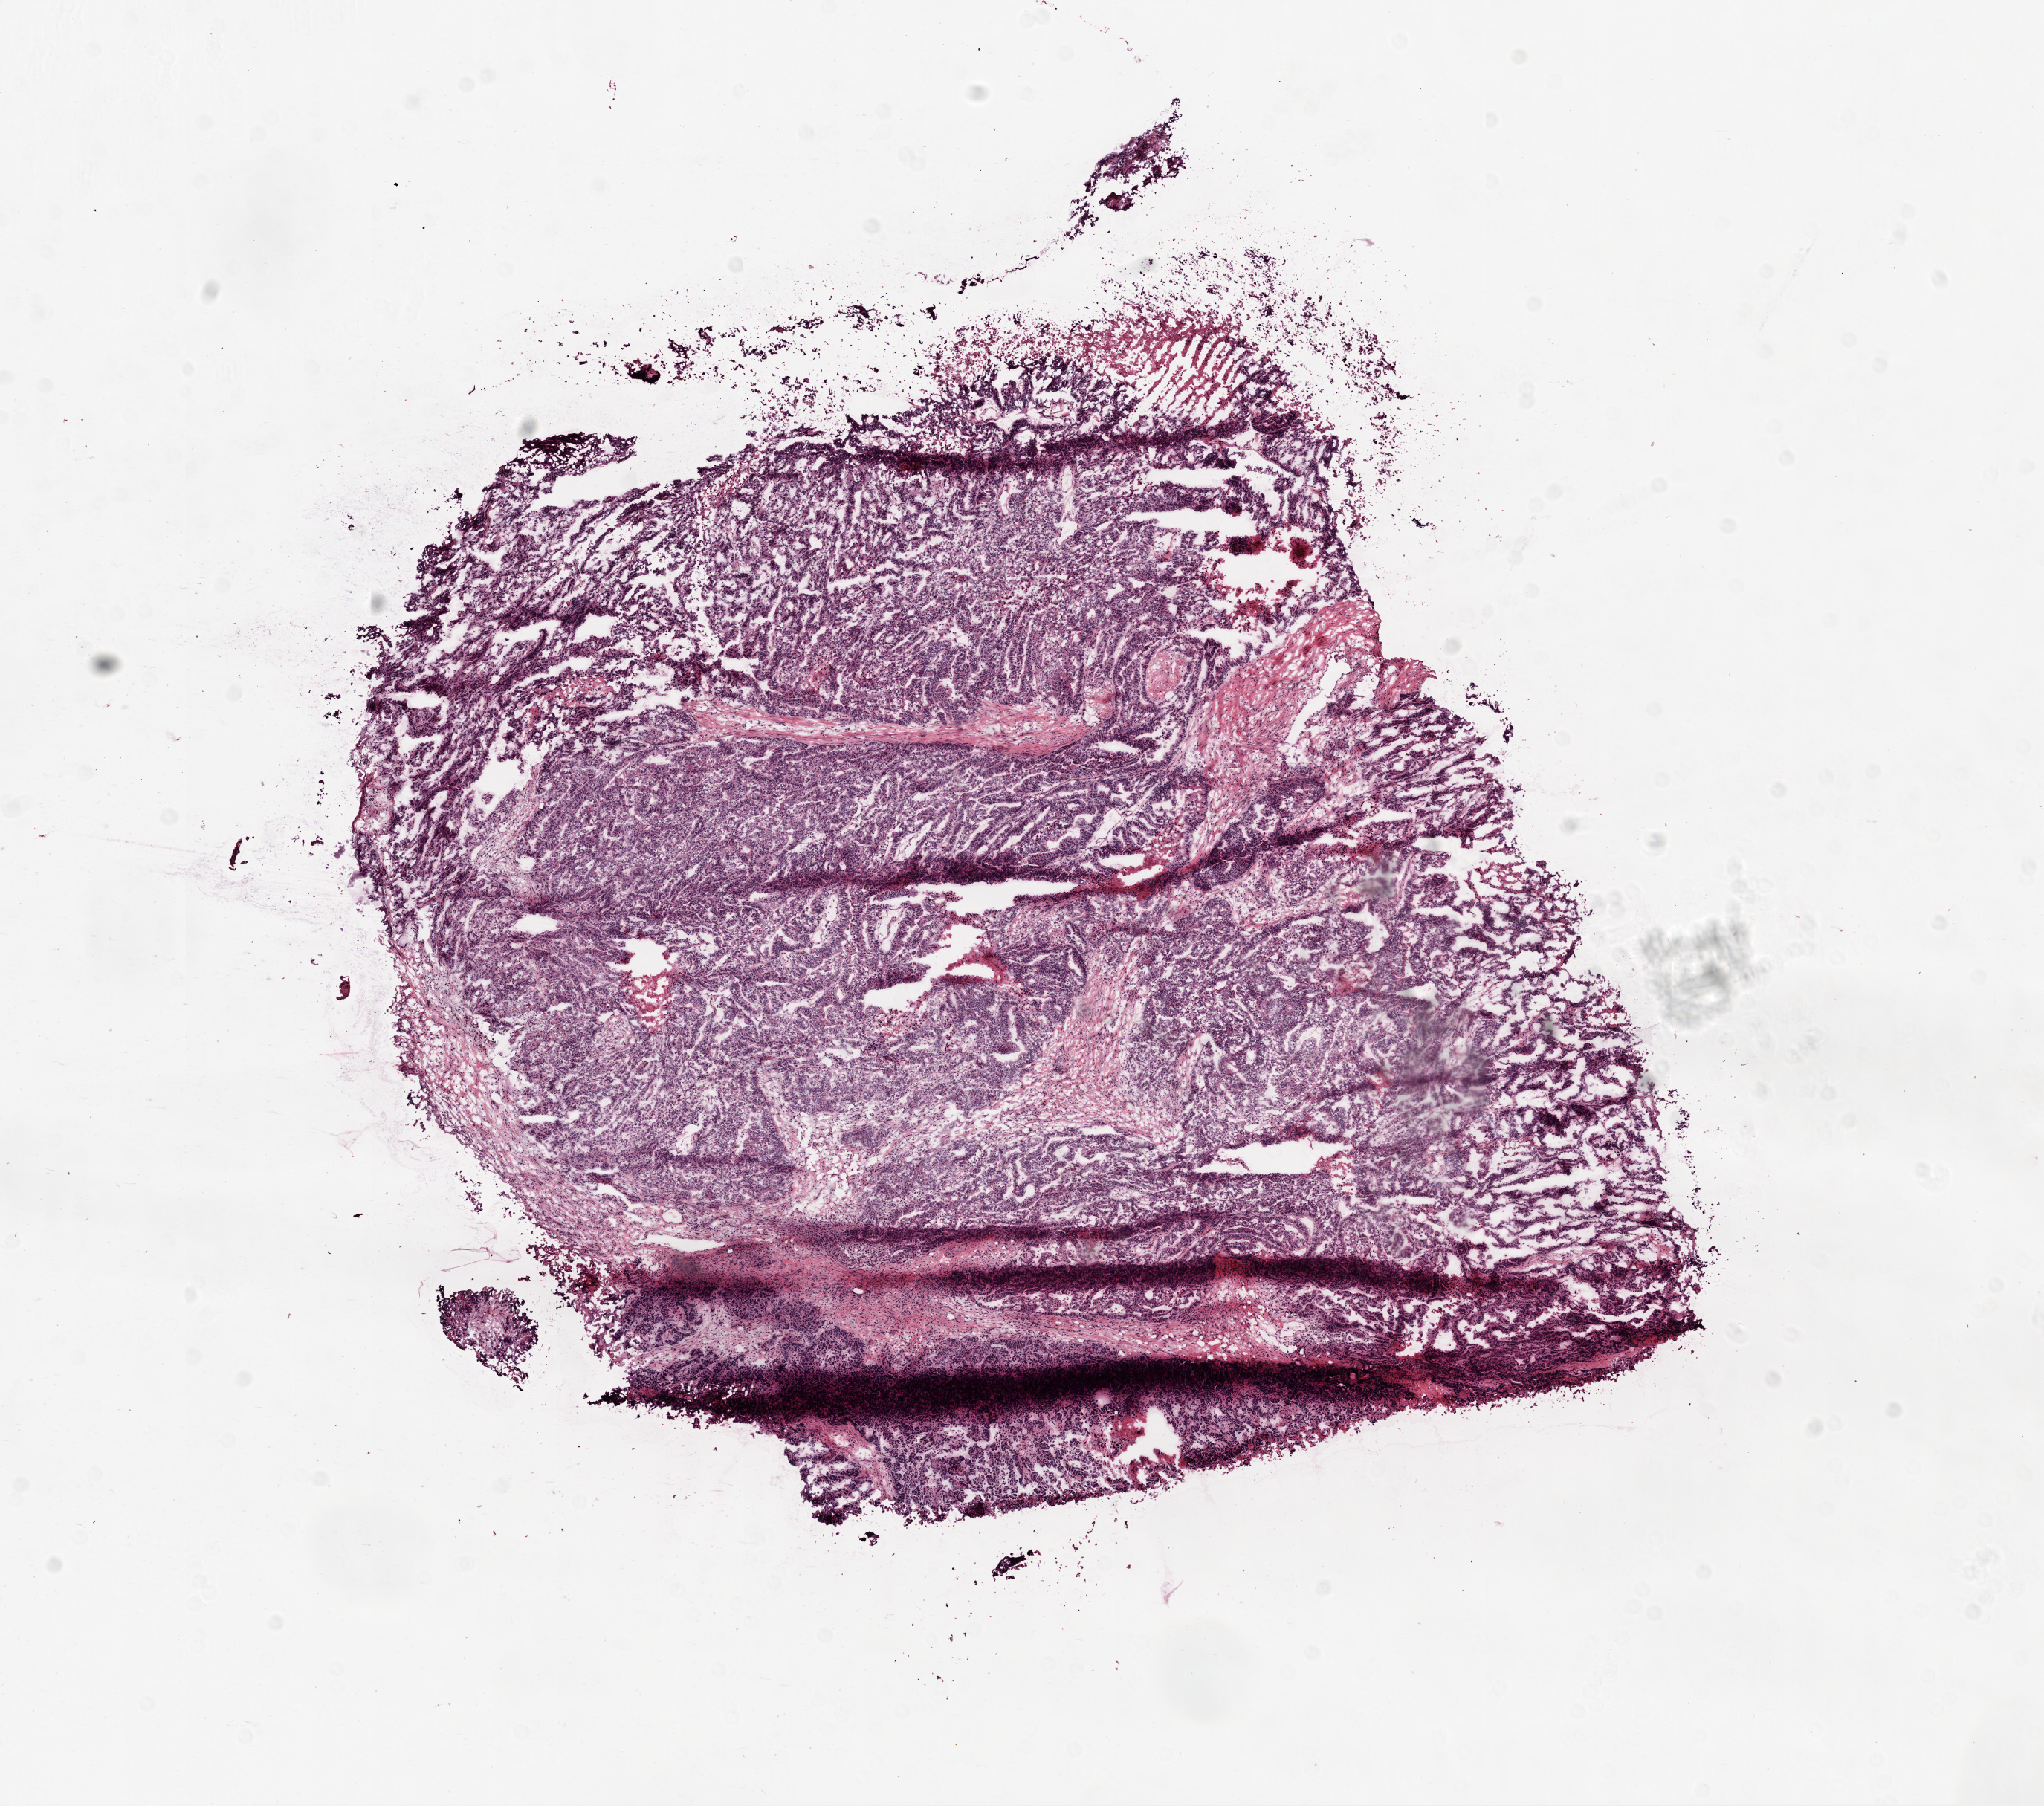
Digitized H&E tissue section (whole slide), low-resolution overview of the scanned area, about 11.0 x 9.7 mm; frozen section from the top of the tissue portion; primary tumour sample from the ovary. Female patient; age at initial diagnosis 80 years.
Histologic diagnosis: Serous cystadenocarcinoma, NOS.